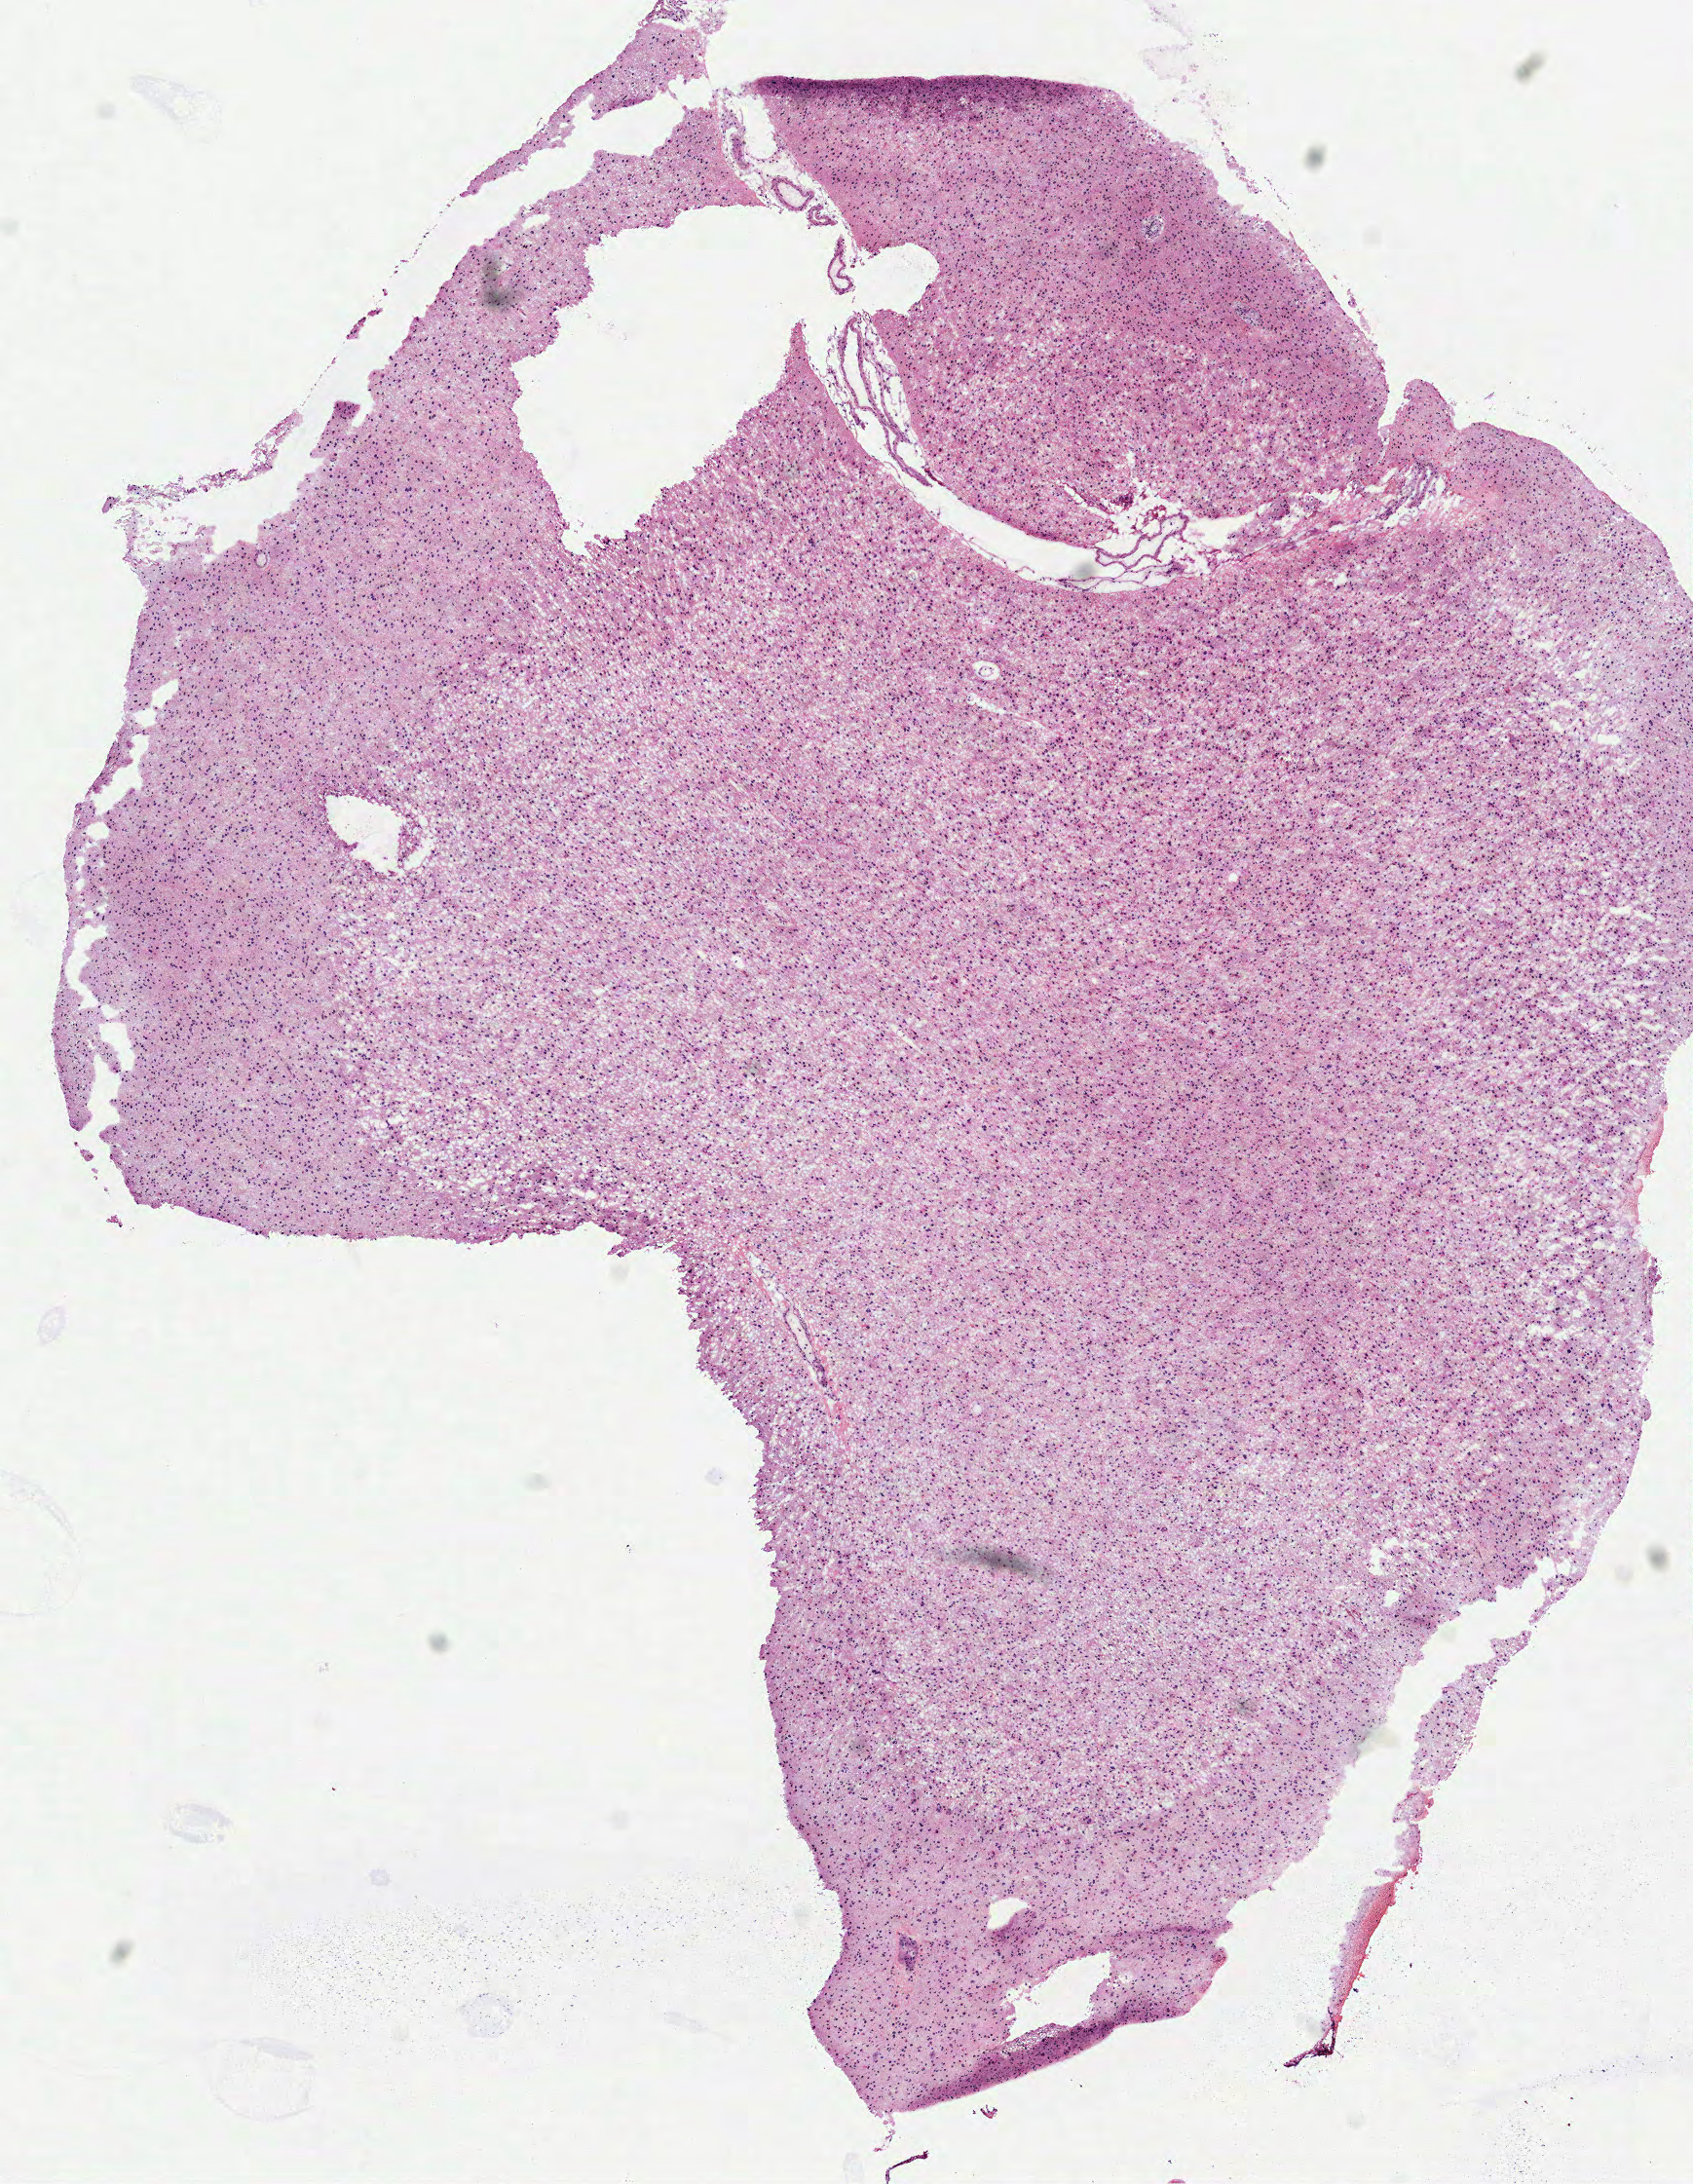
Digitized H&E-stained tissue section (whole slide) — low-resolution overview of the scanned area, about 7.0 x 9.0 mm (slide scanned at 40x). Frozen section from the top of the tissue portion. Brain, primary tumour sample. Male patient; age at initial diagnosis 42 years. Histologic grade: G2 (moderately differentiated). Composition of this section per pathologist review: tumour cells 100%, tumour nuclei 75%, normal cells 0%, stromal cells 0%, necrosis 0%.
• laterality: right
• diagnosis: Astrocytoma, NOS